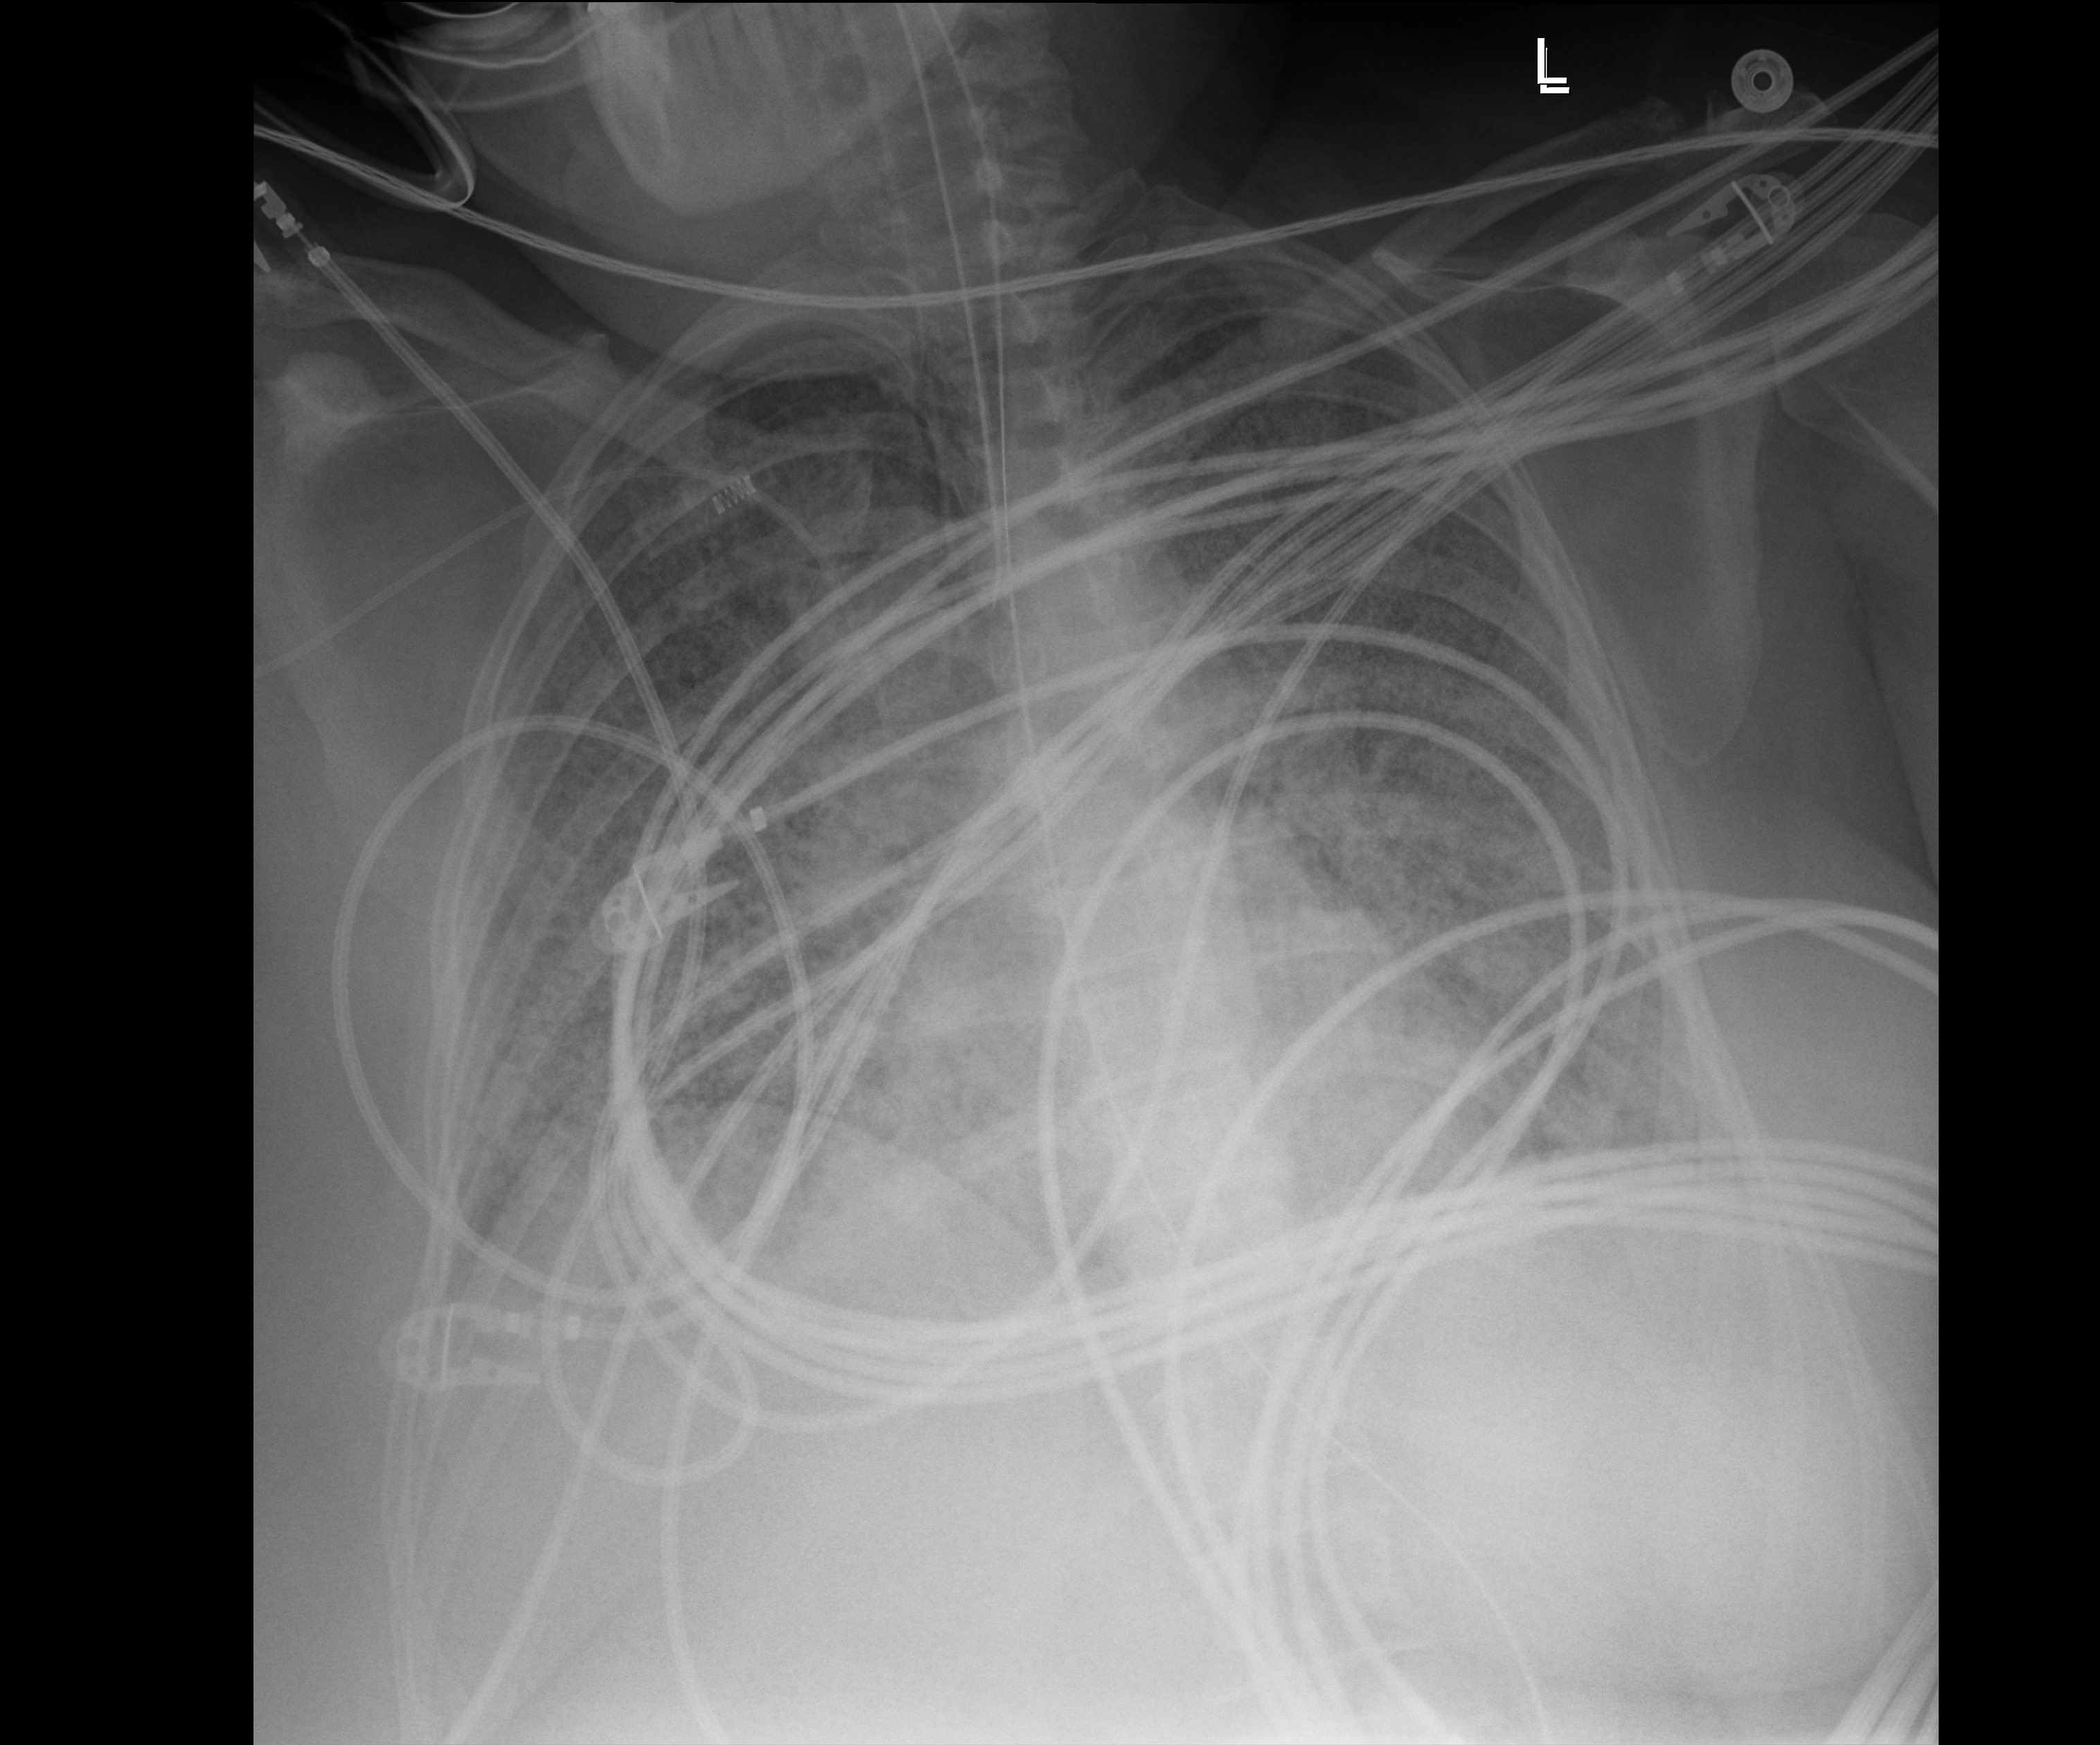
Bedside chest radiograph (digital radiography), anteroposterior (AP) projection. Patient hospitalised with COVID-19; female, aged 18–59 years.
Hospital-stay facts (about this admission, not read from this image; timing relative to this image not recorded): length of hospital stay: 95 days; hypertension (admission record): yes.